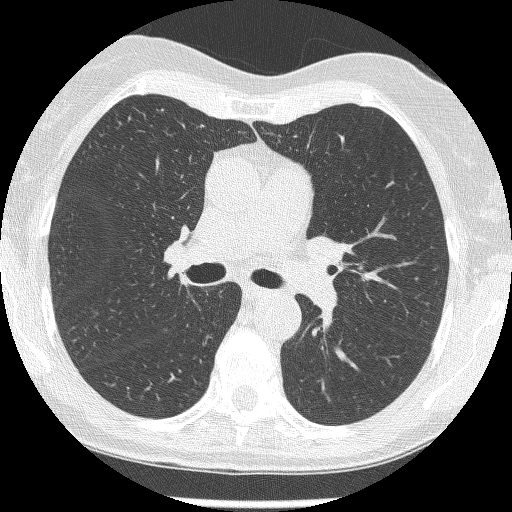
Low-dose screening chest CT, axial slice. Second annual screen. Lung window (W 1500 / L -600 HU). 1.25 mm slice thickness. Female, age 60 years at enrolment. Current smoker at enrolment.
Expert-annotated lung lesion, bounding box <326,137,362,163> (left, top, right, bottom; pixels). The screening reader recorded 2 non-calcified nodules or masses ≥4 mm on this exam; which of them this box marks is not recorded. Official screen result: positive, change unspecified: nodule(s) >= 4 mm or enlarging nodule(s), mass(es), or other non-specific abnormalities suspicious for lung cancer.